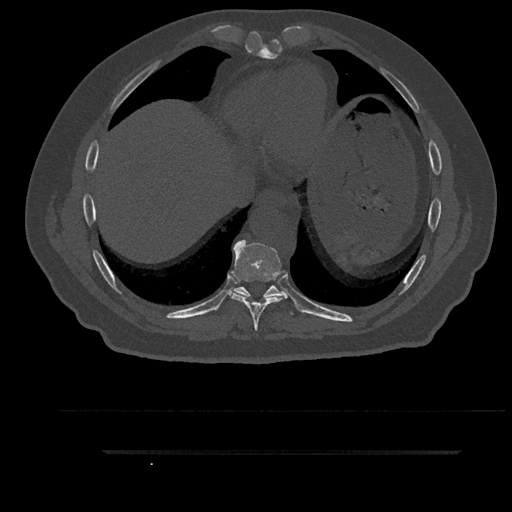
CT including the spine, one axial slice; slice 453 of 797 in the series (ordered by position); reconstruction kernel Br40s/3; bone window (W 1800 / L 400 HU); 0.5 mm slice thickness; 512 × 512 image matrix, field of view 432 × 432 mm. Patient: male, 63 years. Case-level facts recorded for this patient, not image findings: primary cancer: renal; vertebrae with lytic lesions (as recorded): T8.
Outlined on this slice (semi-automatic segmentation, software-assisted and operator-edited):
- T8 vertebra: box from (x=230, y=240) to (x=287, y=331) px
- T9 vertebra: (x=232, y=285)–(x=292, y=314)